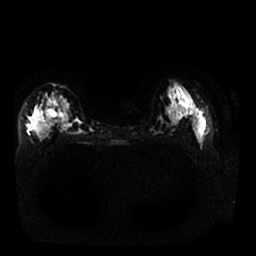
Breast MRI, one axial slice. Position 11 of 25 along the scan axis. Diffusion-weighted series; image 2 of 4 stored at this slice position (different b-values; order by instance number). 1.5 T. 256 × 256 image matrix, field of view 340 × 340 mm. Female patient.
Outlined on this slice (manually delineated by an expert):
- tumour on diffusion-weighted imaging: bounding box [x1, y1, x2, y2] px = [31, 109, 45, 137]